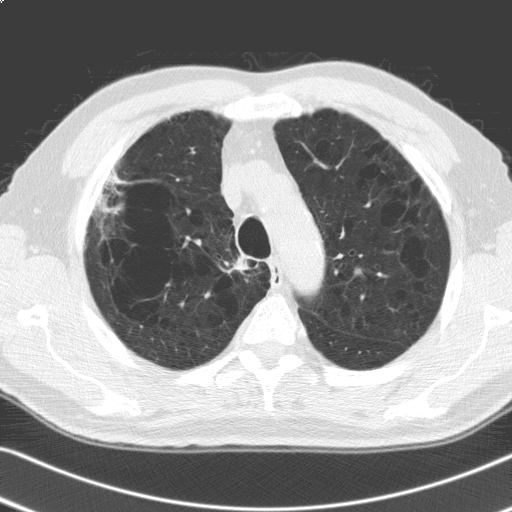
Axial slice from a low-dose chest CT screening exam. Second screening round (one year after baseline). Lung window (W 1500 / L -600 HU). 3.2 mm slice thickness. Standard (soft-tissue) reconstruction kernel (C). 512 × 512 image matrix, field of view 336 × 336 mm. Male, age 69 years at enrolment.
Expert reader's lesion annotation, box from (x=88, y=165) to (x=134, y=221) px. The screening reader recorded 6 non-calcified nodules or masses ≥4 mm on this exam; which of them this box marks is not recorded. Participant outcome: lung cancer diagnosed 91 days after this screen — adenosquamous carcinoma, right upper lobe, poorly differentiated (G3), stage IV (AJCC 6th edition), 30 mm at pathology.